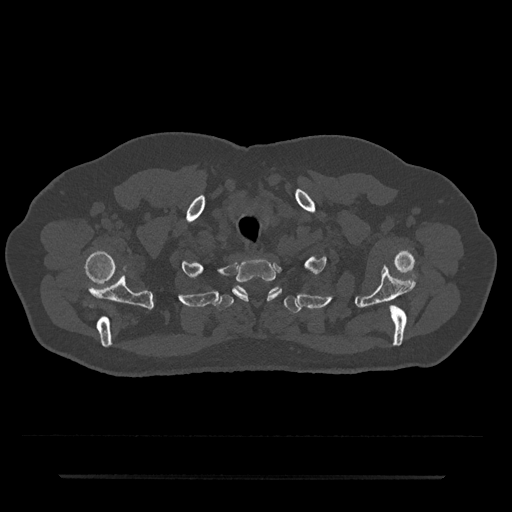
CT including the spine, one axial slice; position 628 of 797 along the scan axis; 120 kVp; bone window (W 1800 / L 400 HU); 0.5 mm slice thickness; 512 × 512 image matrix, field of view 437 × 437 mm. Patient: male, 69 years. Case-level facts recorded for this patient, not image findings: primary cancer: prostate.
Structures marked on this image (semi-automatic segmentation, software-assisted and operator-edited):
- T1 vertebra: bounding box [x1, y1, x2, y2] px = [233, 258, 282, 300]
- T2 vertebra: [216, 286, 301, 313]